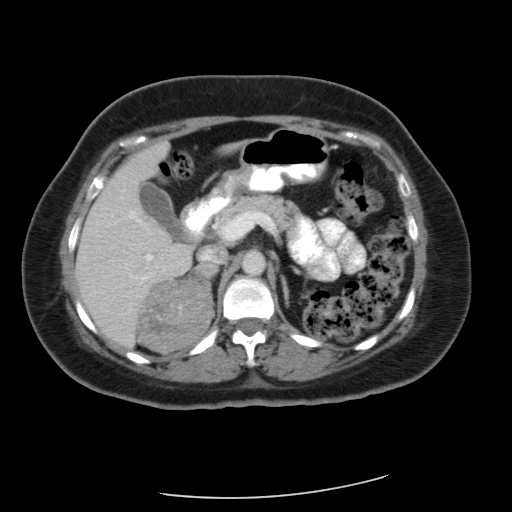
Contrast-enhanced abdominal CT, one axial slice. Position 36 of 56 along the scan axis. Soft-tissue window (W 400 / L 40 HU). 5 mm slice thickness. 512 × 512 image matrix, field of view 400 × 400 mm. Patient: female, 58 years. From the clinical record (not read from this slice): diagnosis: adrenocortical carcinoma; tumour side: right adrenal; tumour size at pathology: 9 cm; Ki-67 index: 25 %.
Annotated regions visible in this slice (semi-automatic segmentation, software-assisted and operator-edited):
- mass: bounding box [x1, y1, x2, y2] px = [140, 265, 215, 353]